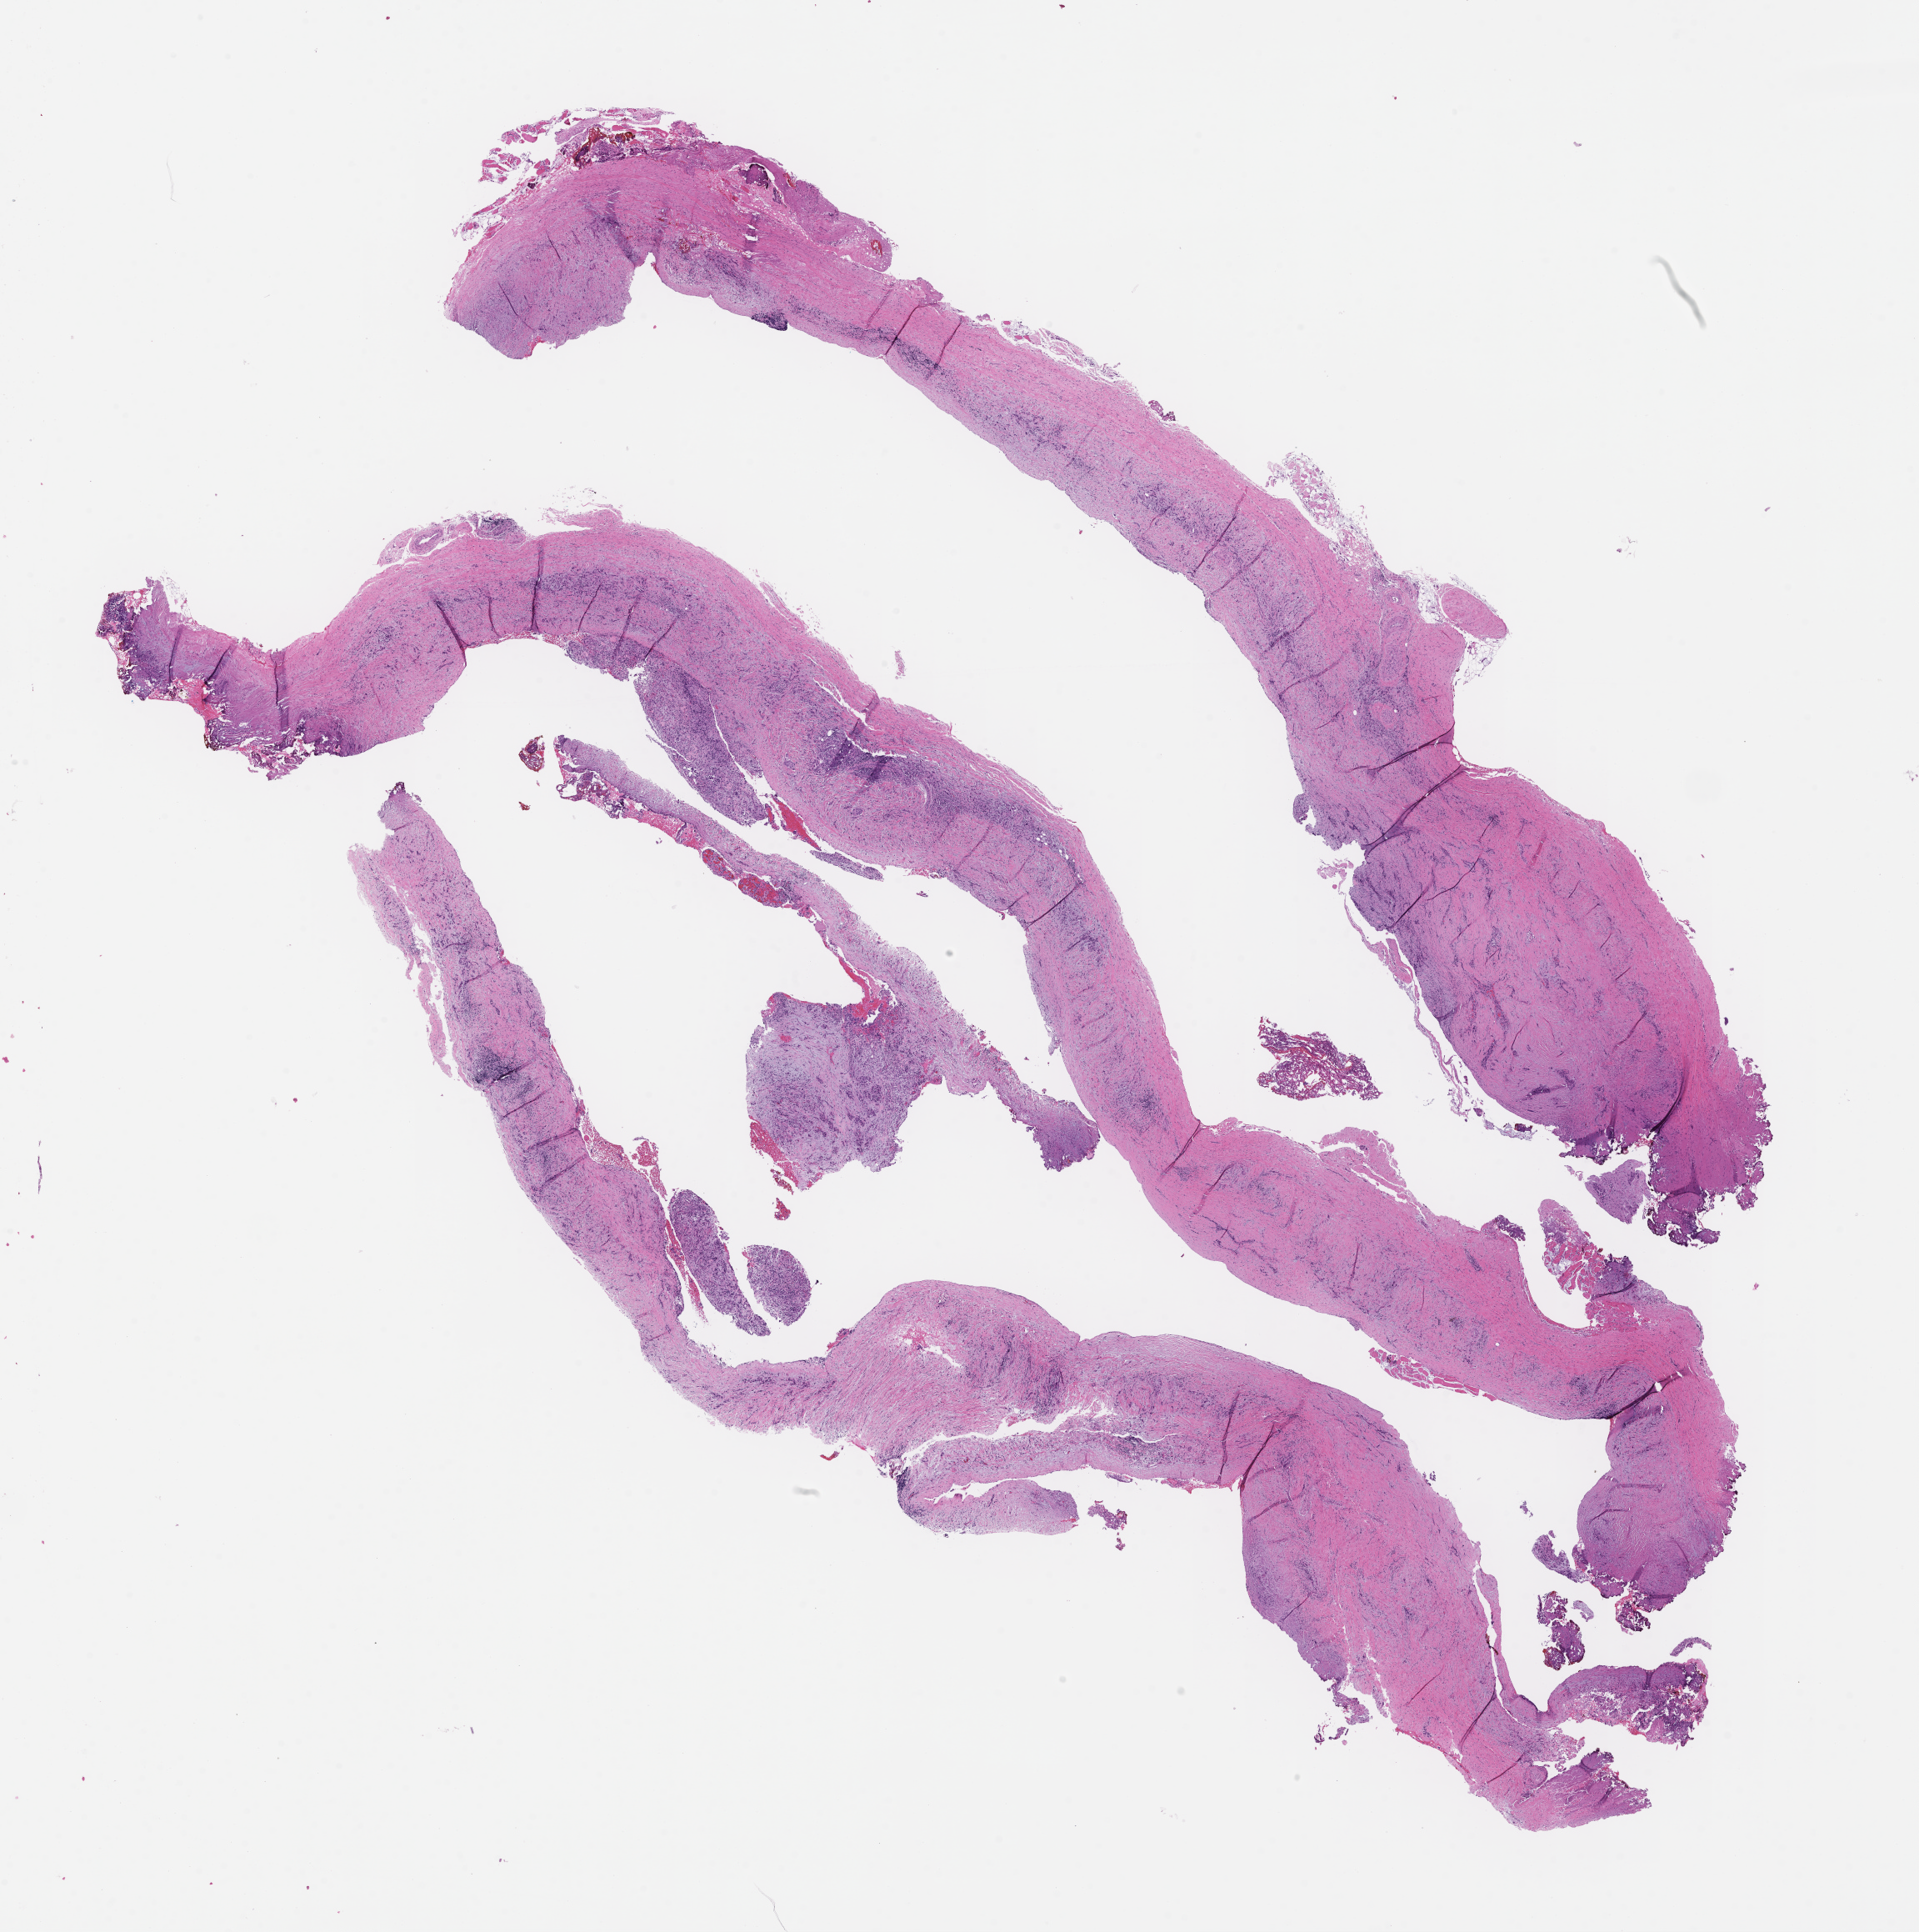
Haematoxylin and eosin whole-slide image — a low-resolution overview of the entire scanned area, about 18.6 x 18.7 mm, formalin-fixed paraffin-embedded section, specimen time point: archival tissue. Patient sex: female.
This section: metastatic tumor tissue. Primary diagnosis of the patient: Non-Small Cell Lung Carcinoma.